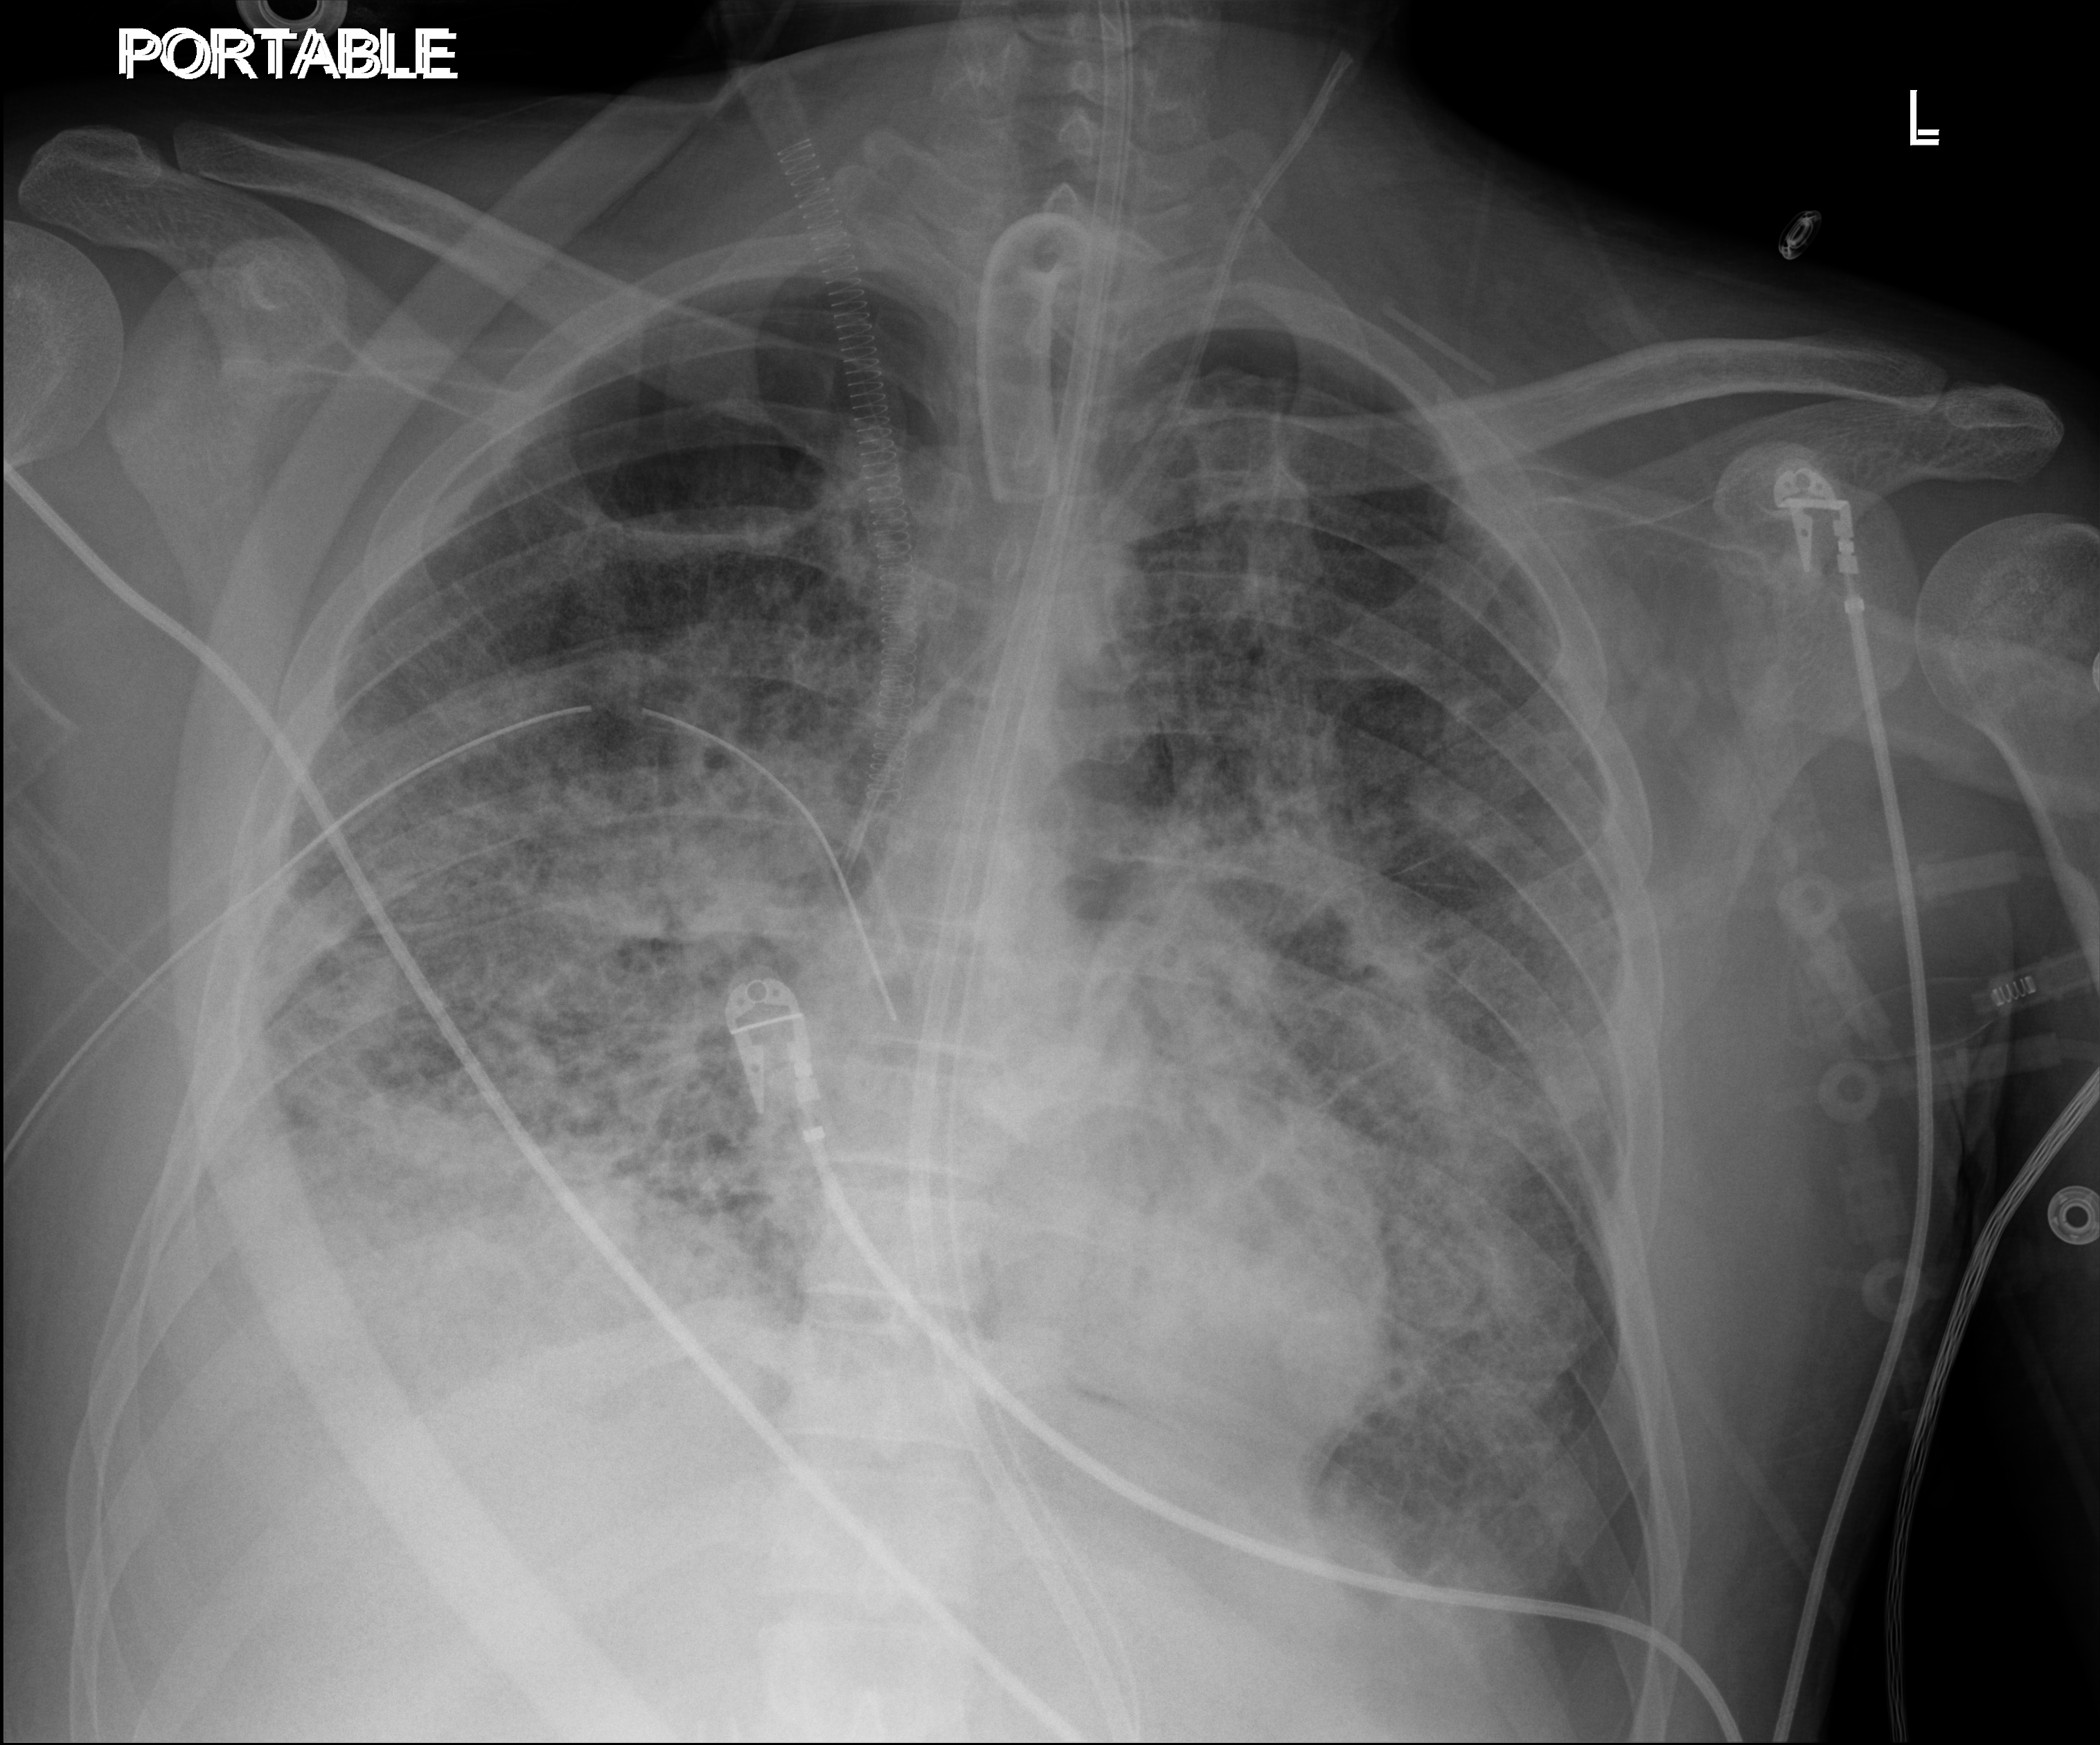
Chest X-ray (portable). Patient hospitalised with COVID-19, aged 18–59 years.
Hospital-stay facts (about this admission, not read from this image; timing relative to this image not recorded):
- admitted to intensive care during this hospital stay: yes
- mechanically ventilated during this hospital stay: yes